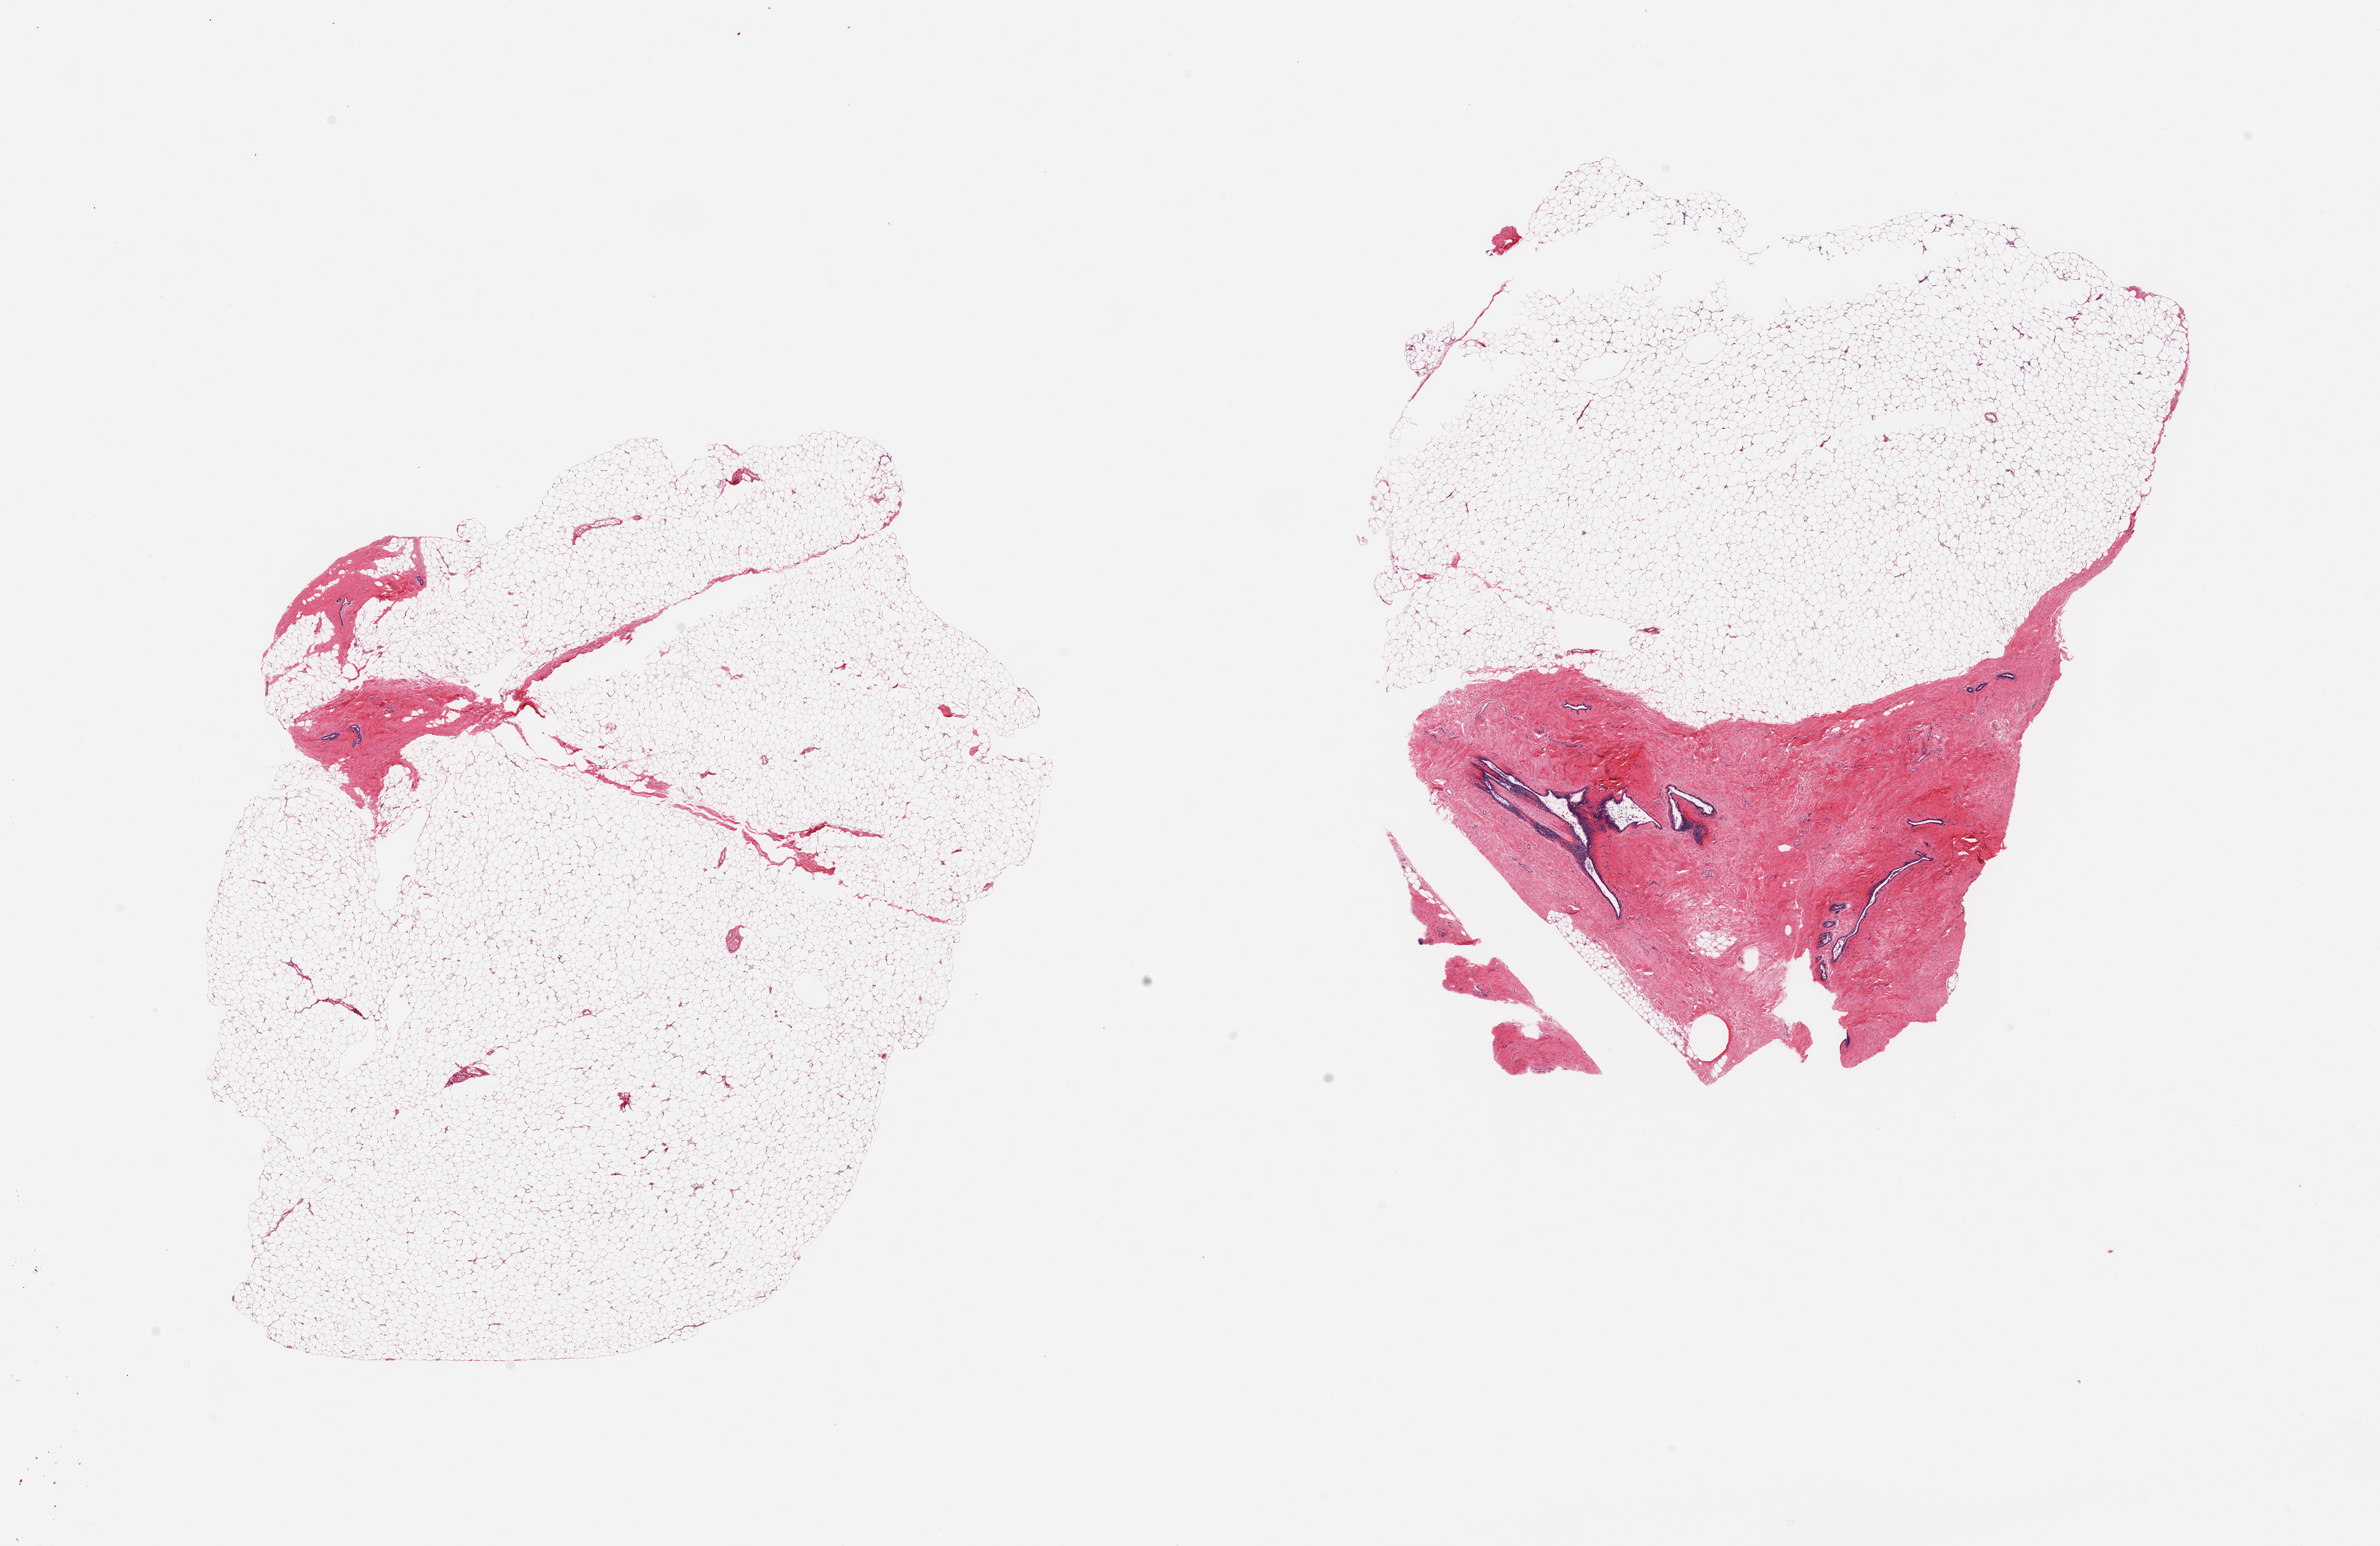
Haematoxylin and eosin whole-slide image — low-resolution overview of the scanned area, about 24.6 x 16.0 mm (from a 20x scan), PAXgene-fixed paraffin-embedded (PFPE) section, target tissue: breast, tissue donor sample. Donor sex: male.
- pathologist's review note for this sample: 2 pieces; mature adipose tissue and dense fibrotic stroma with ductal structures, suggestive of gynecomastoid stromal and ductal hyperplasia